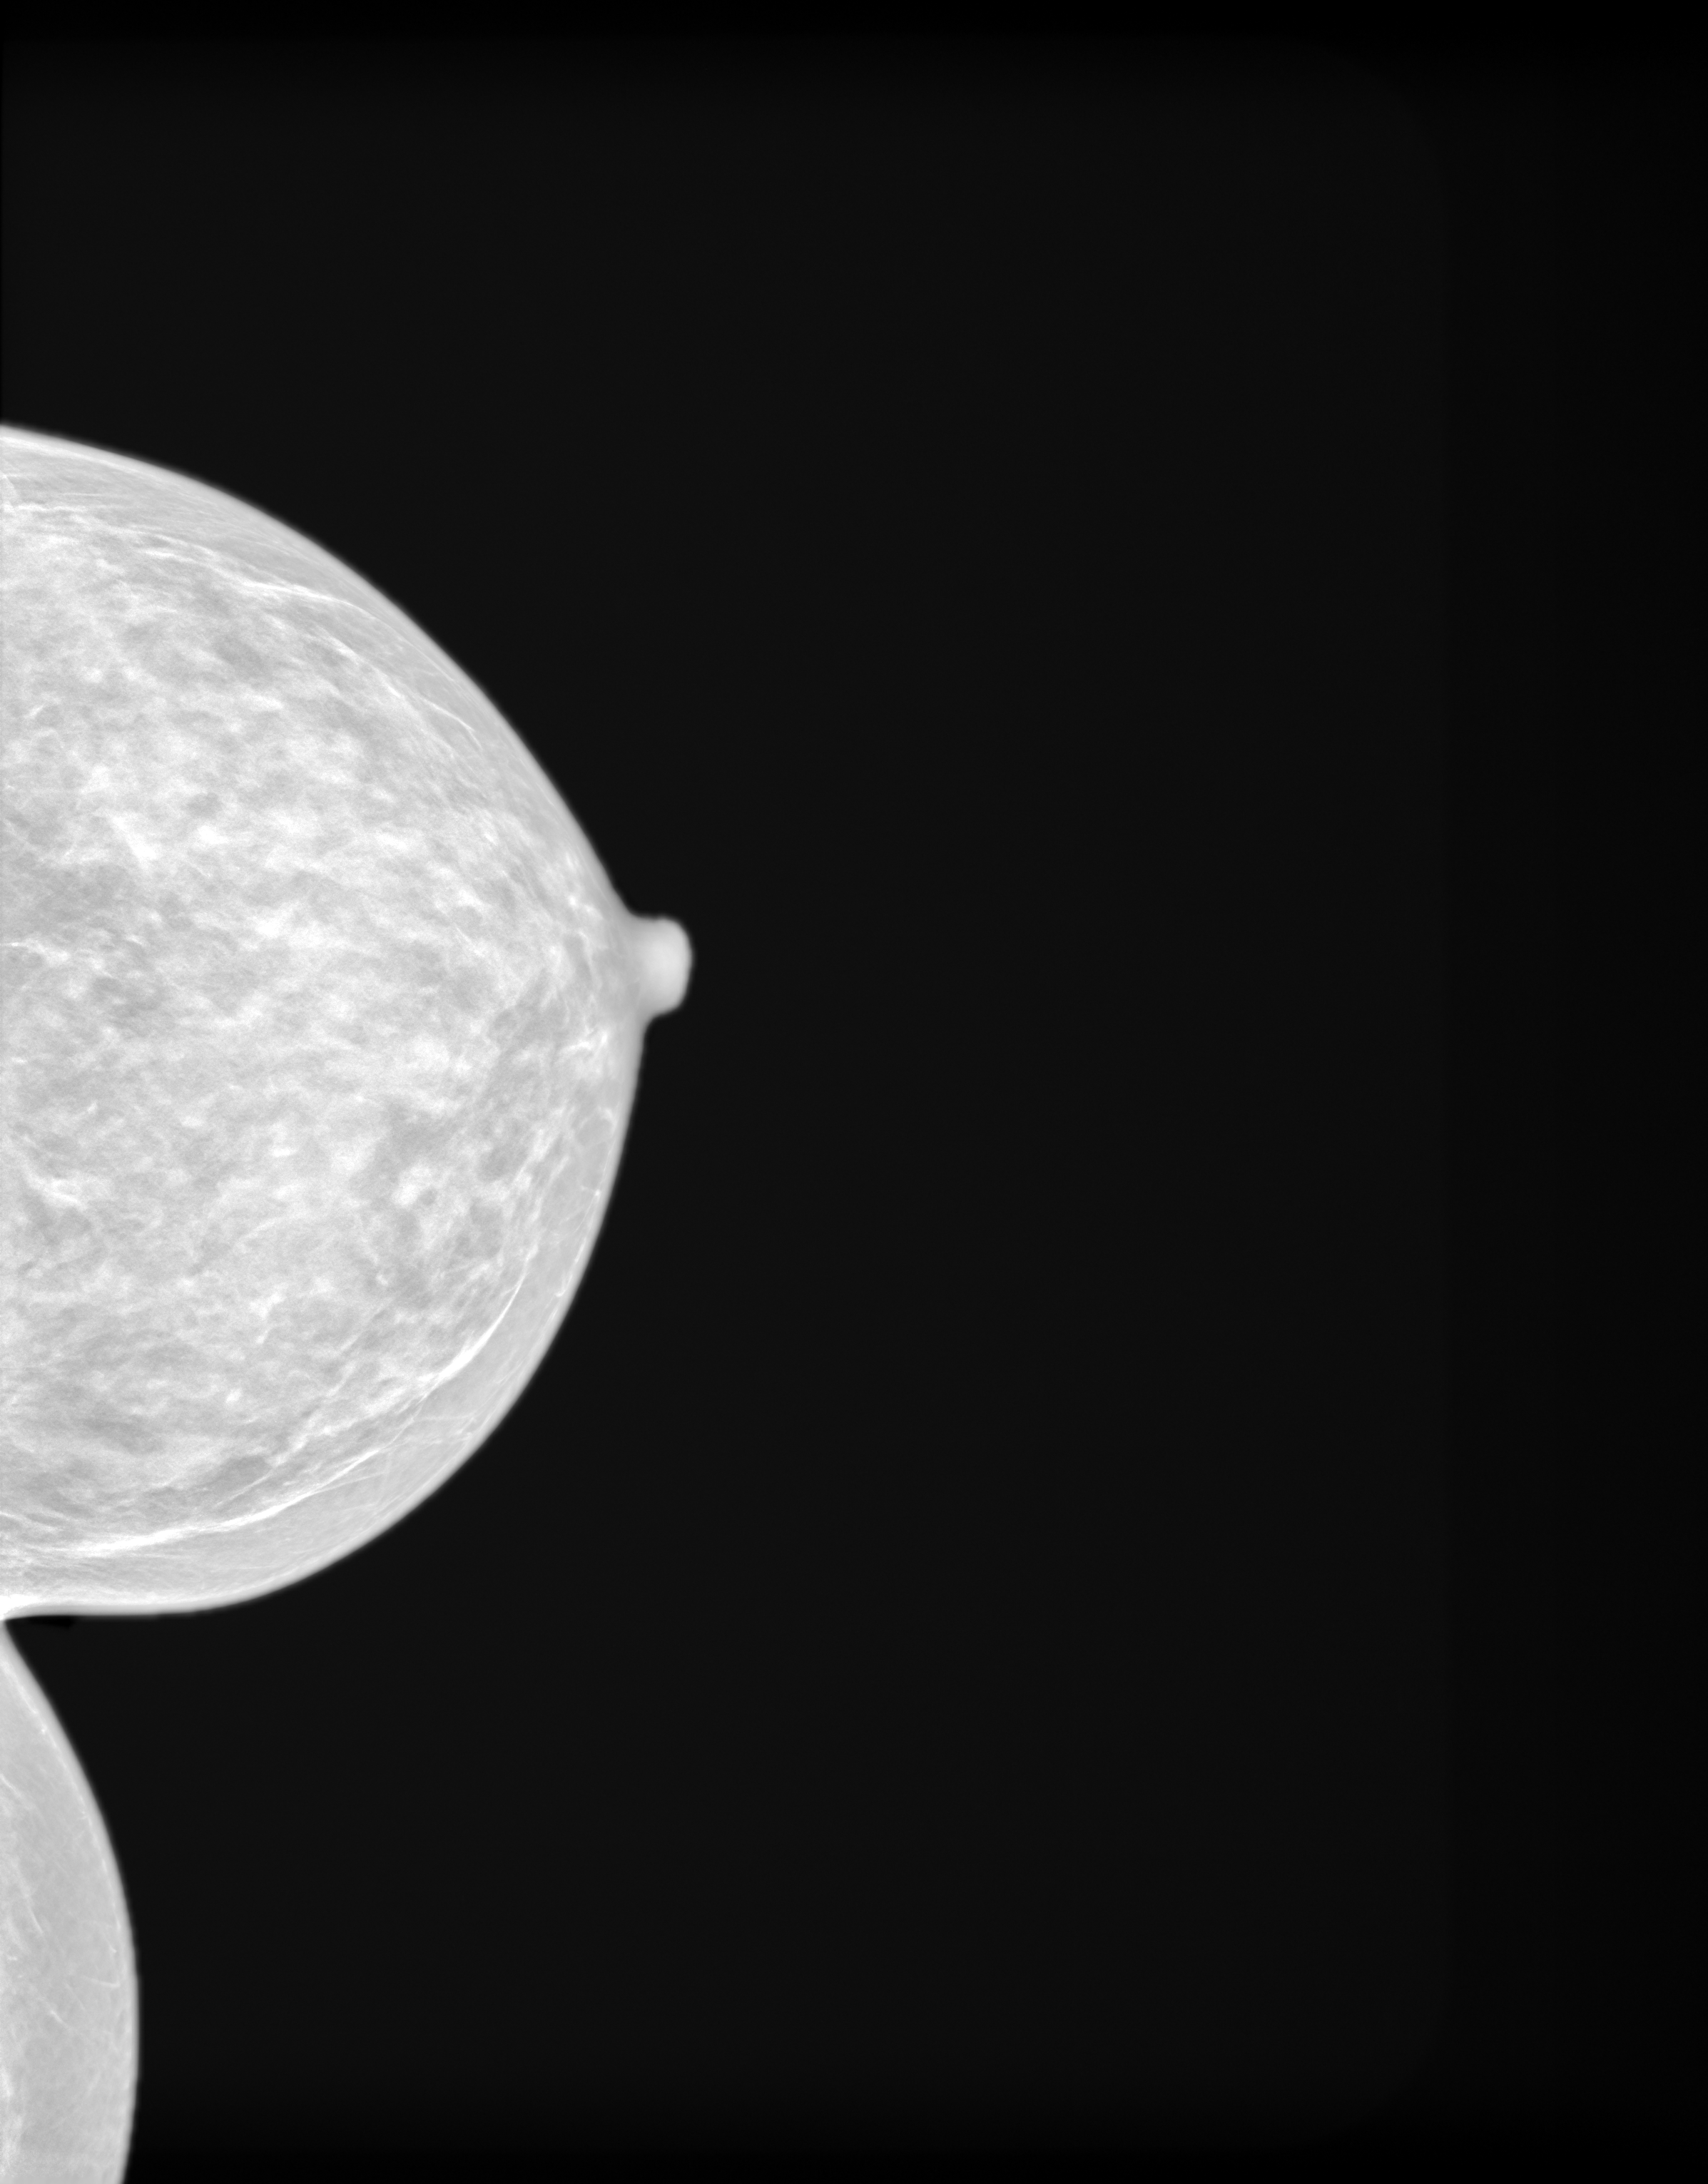
Screening examination. Patient aged 61 years (female).
Image type: synthesized 2-D view from tomosynthesis. Breast: left. Projection: cranio-caudal projection.